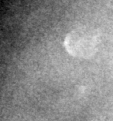
Crop from a digitized film mammogram around one marked abnormality; right breast; MLO view.
Calcifications, morphology lucent center; BI-RADS assessment category 2; subtlety rating 3 on a 1 (subtle) to 5 (obvious) scale; benign without callback (not worked up further).